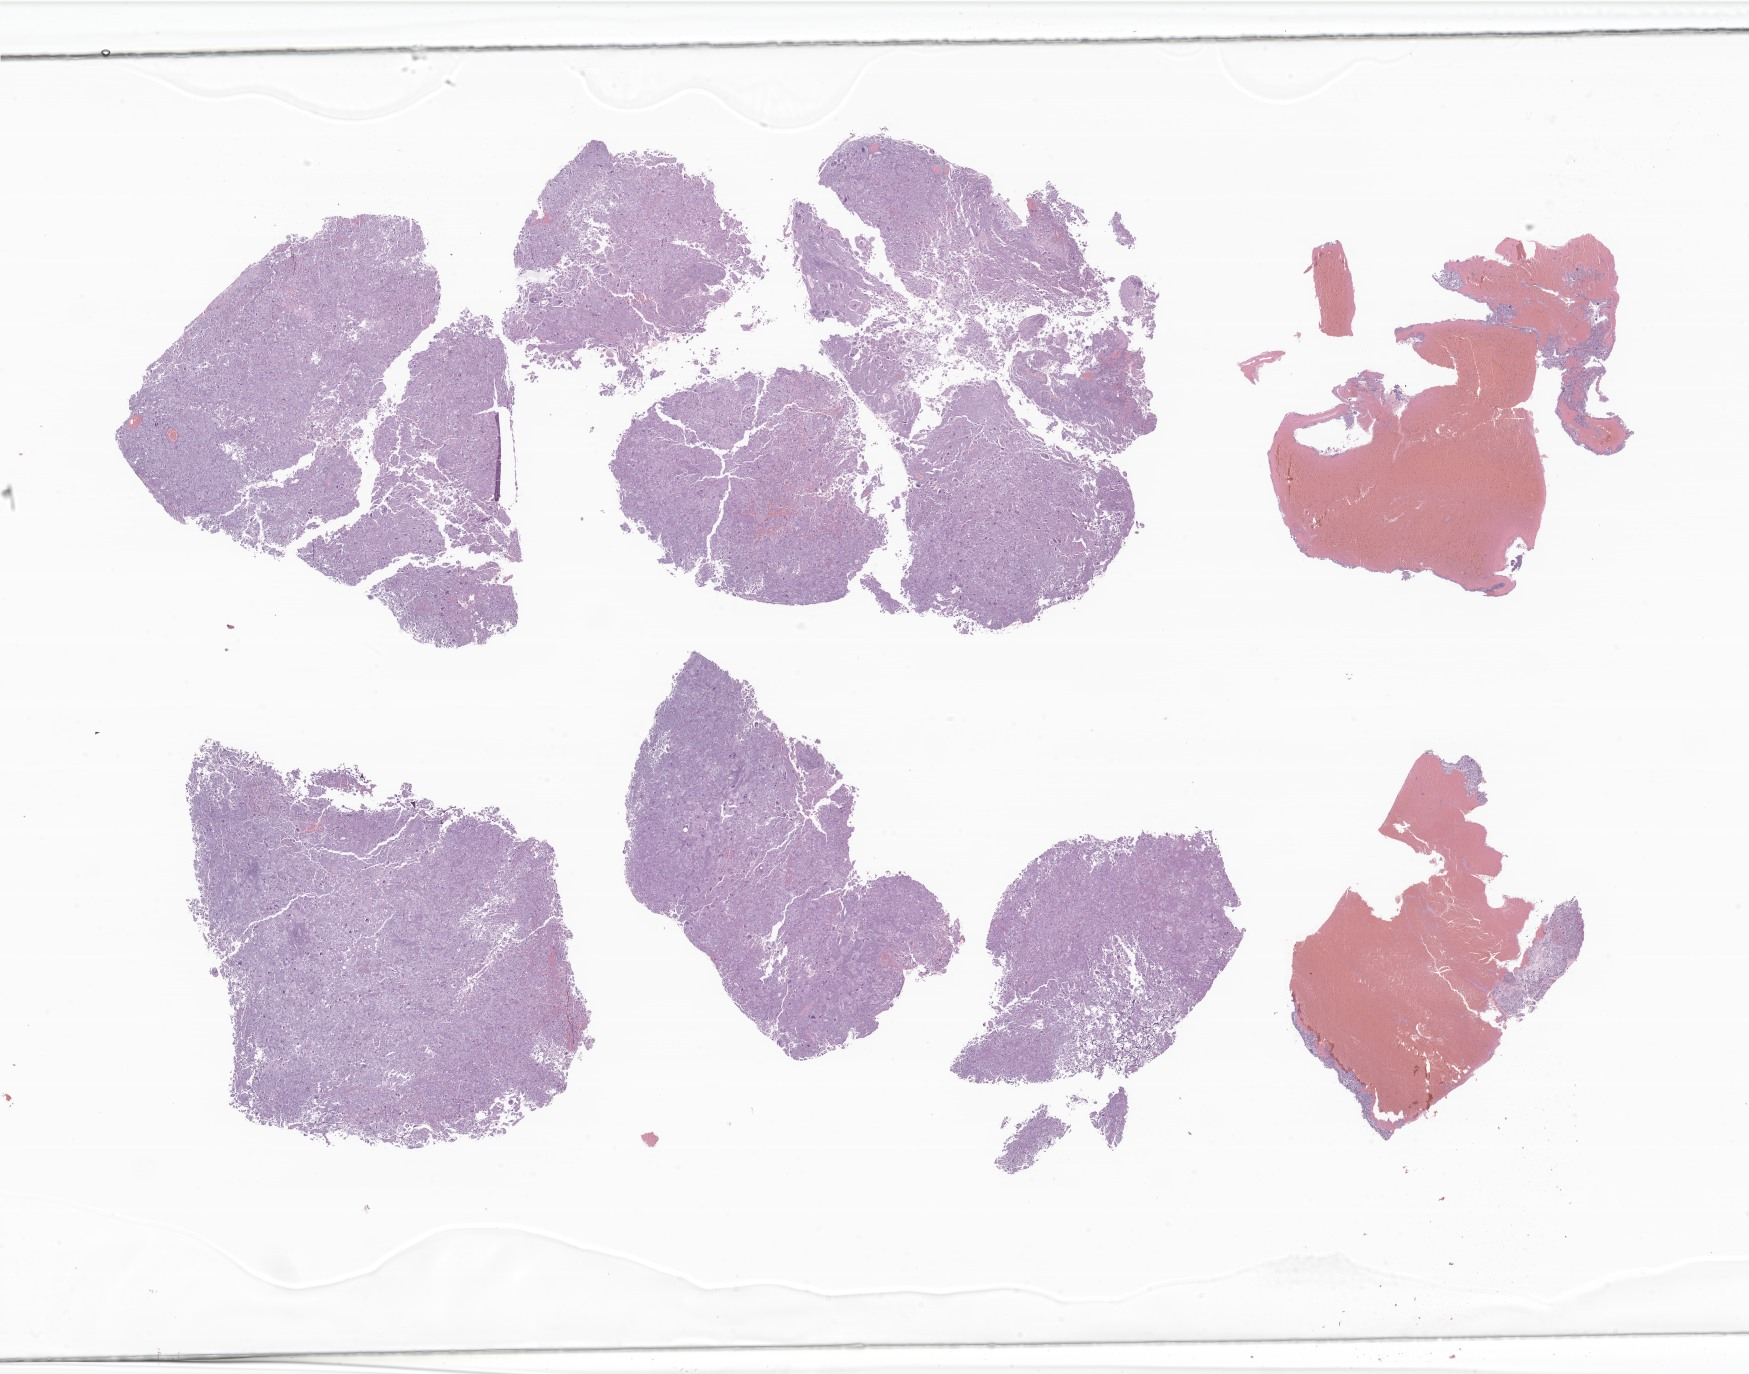
Hematoxylin and eosin (H&E) whole-slide image of tumor tissue from the brain, whole scanned area (about 29.5 x 23.2 mm) shown as a low-resolution overview, FFPE section. Patient: male, age 126 months (10 years 6 months).
Recorded diagnosis: Glioma, malignant.